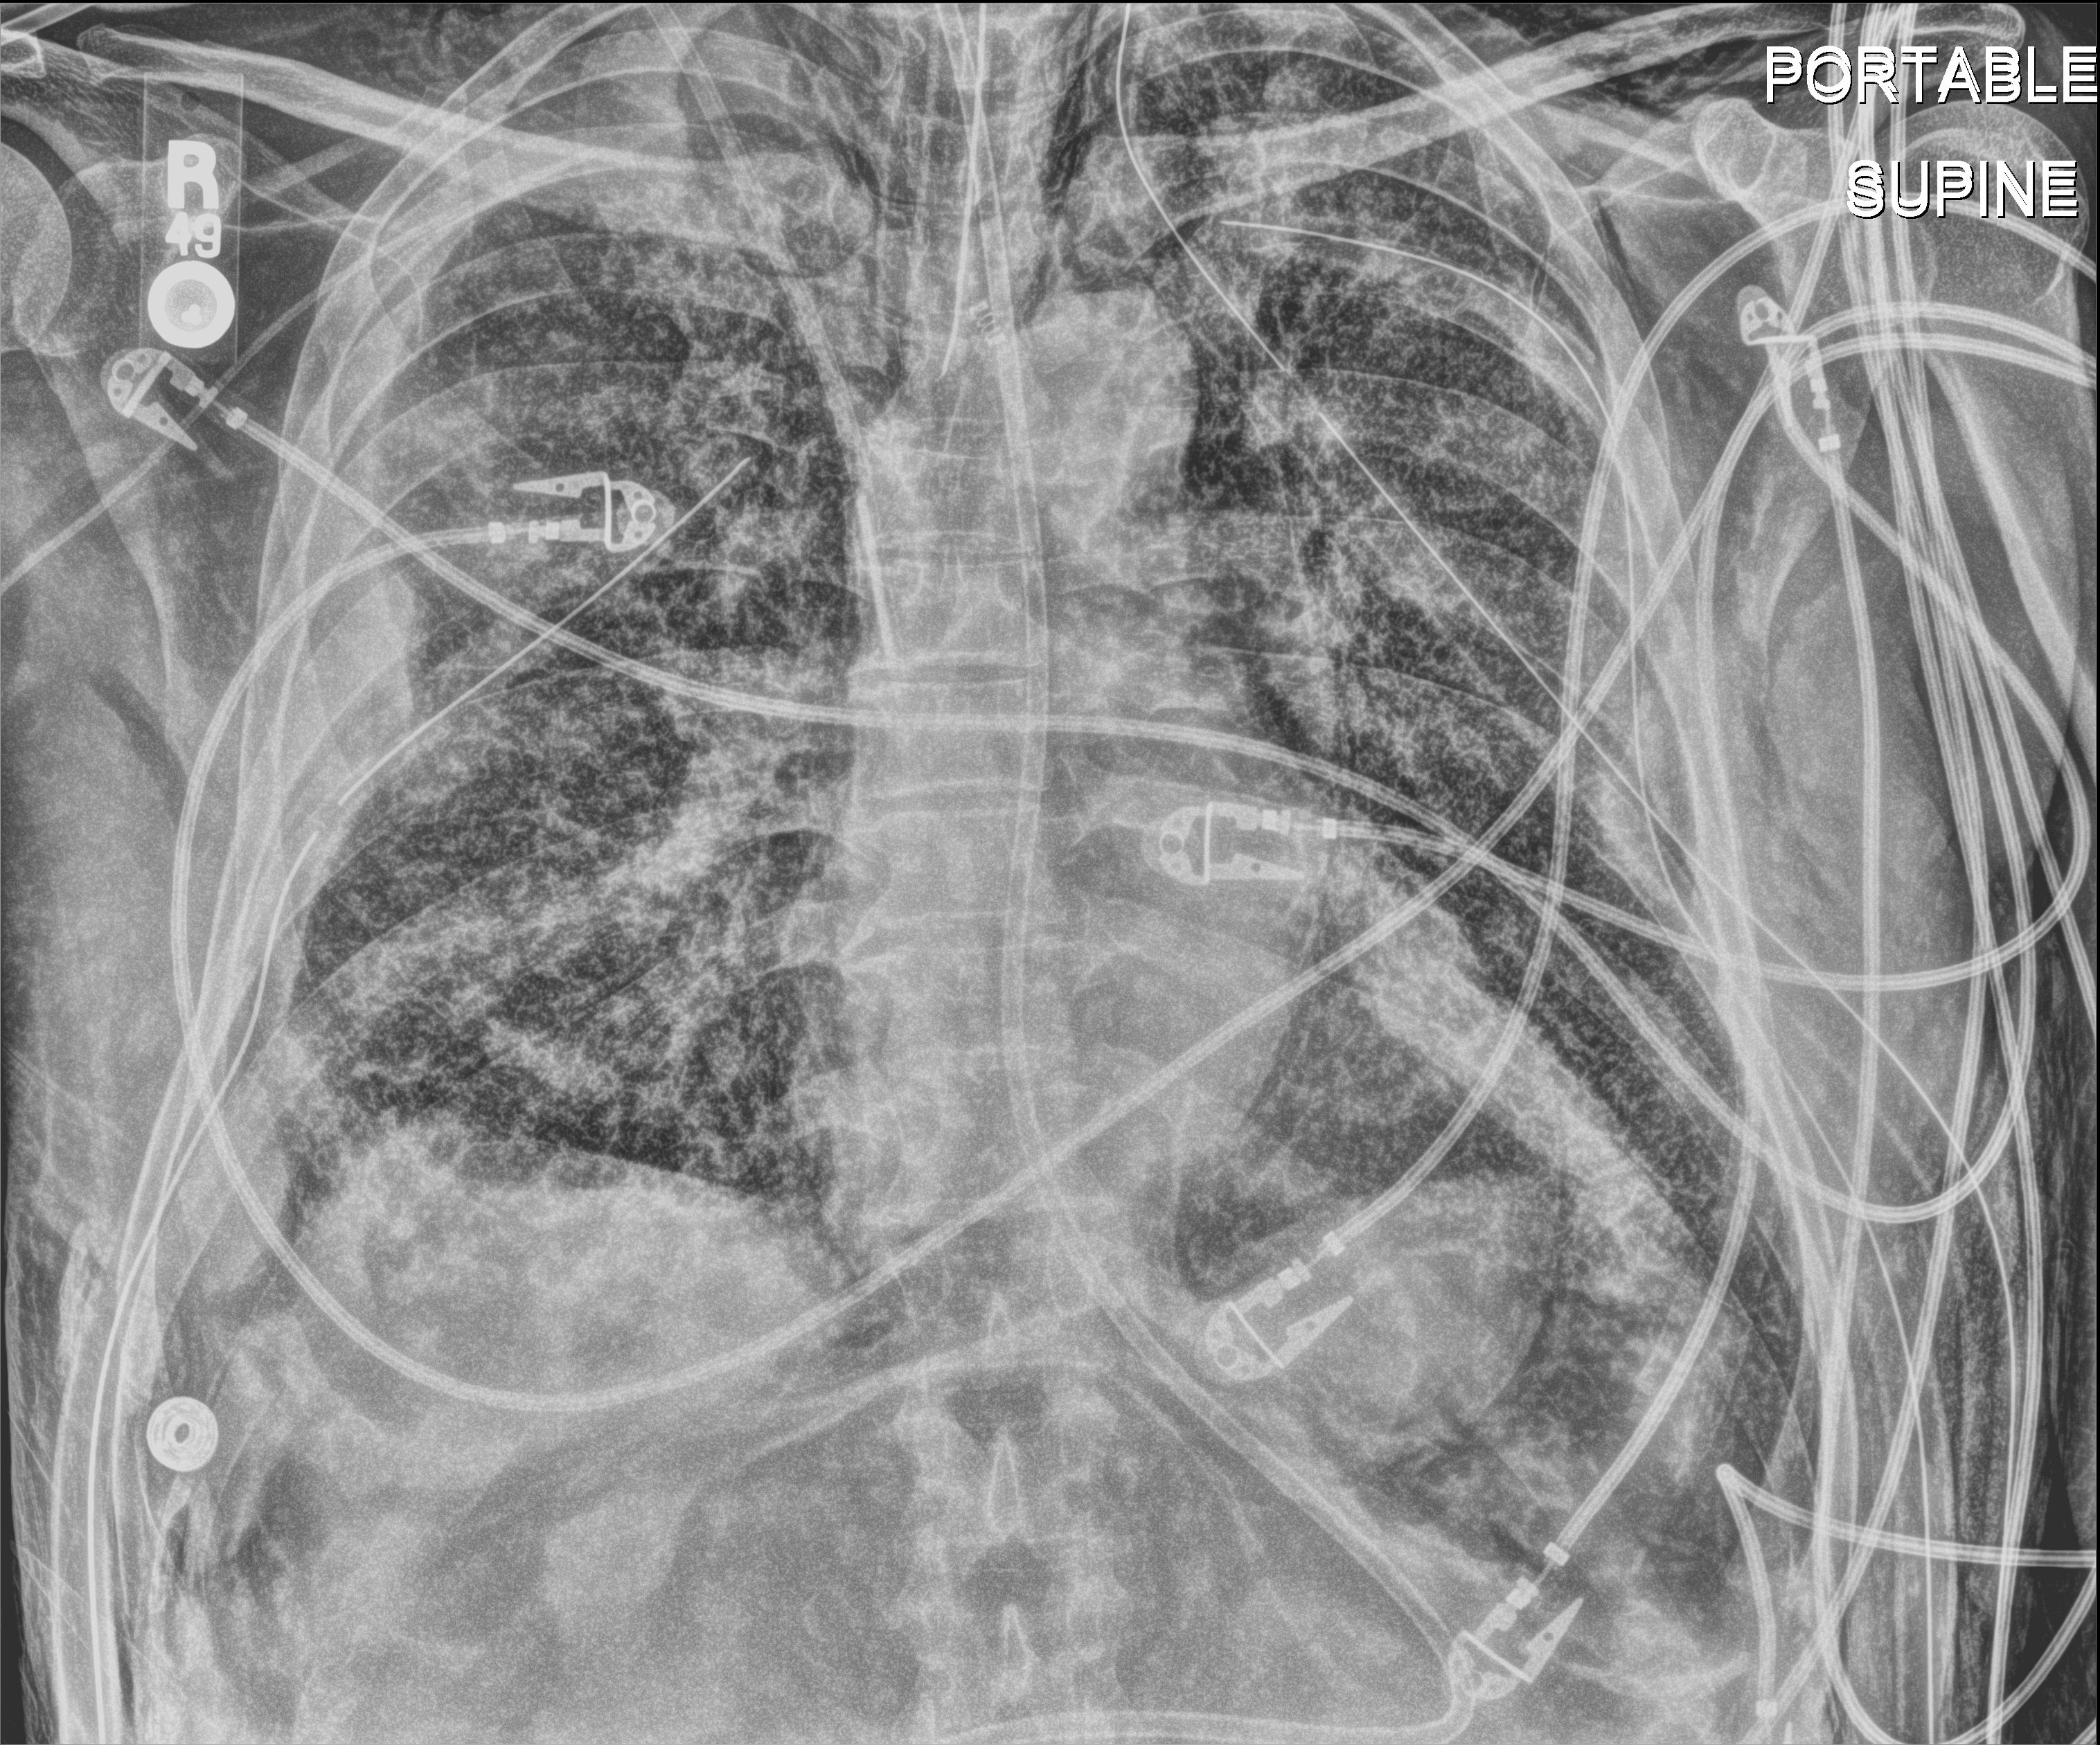
Bedside chest radiograph (digital radiography), anteroposterior (AP) projection. Patient hospitalised with COVID-19; male, aged 18–59 years.
Admission-level facts for this patient (not findings on this image; timing relative to this image not recorded):
- chronic kidney disease (admission record): no
- admitted to intensive care during this hospital stay: yes
- mechanically ventilated during this hospital stay: yes